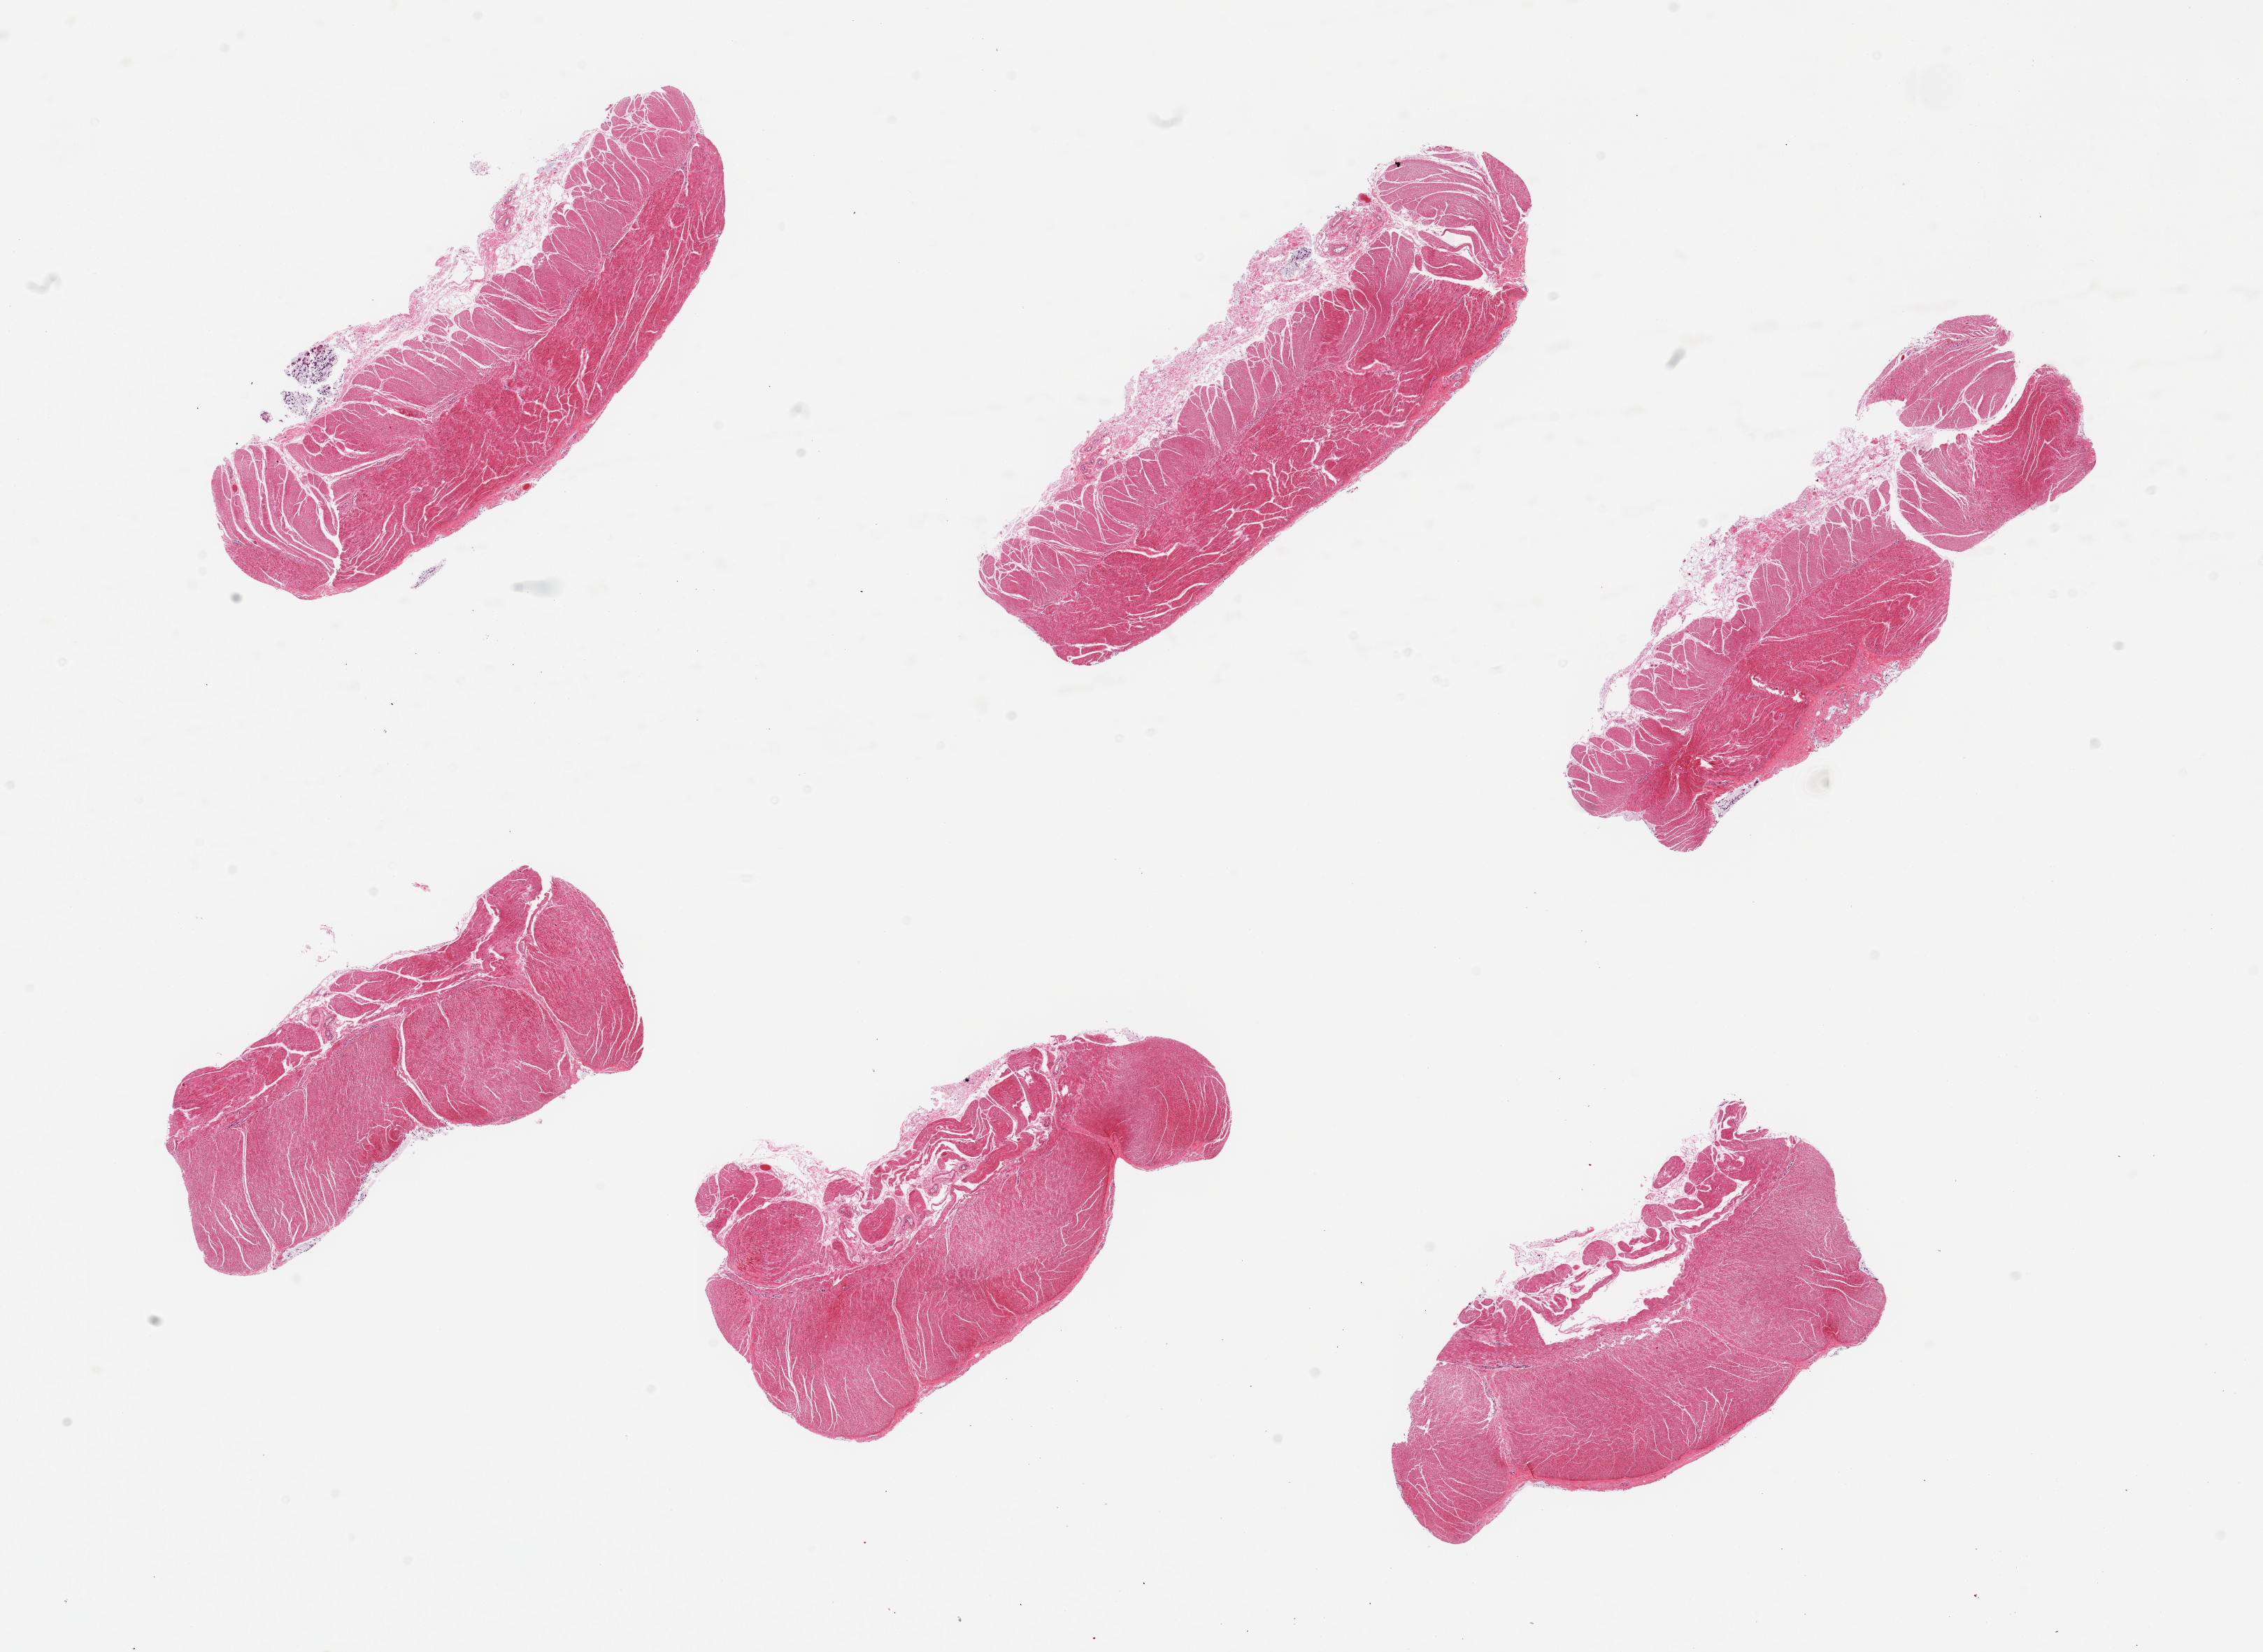
Hematoxylin and eosin (H&E) whole-slide image, brightfield — shown as a low-resolution overview of the whole scanned area (about 25.6 x 18.7 mm), PAXgene-fixed, paraffin-embedded tissue, target tissue: sigmoid colon, tissue donor sample. Donor: female.
* review note (as recorded): 6 pieces